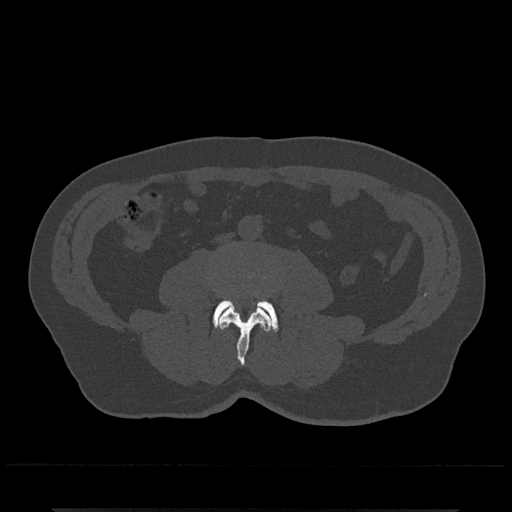
CT including the spine, one axial slice. Slice 193 of 797 in the series (ordered by position). Reconstruction kernel Br40s/3. 120 kVp. Bone window (W 1800 / L 400 HU). 0.5 mm slice thickness. 512 × 512 image matrix, field of view 393 × 393 mm. Patient: male, 67 years. From the clinical record (not read from this slice): primary cancer: prostate.
Annotated regions visible in this slice (semi-automatic segmentation, software-assisted and operator-edited):
- L3 vertebra: bounding box (x1, y1, x2, y2) in pixels: (218, 306, 272, 365)
- L4 vertebra: (213, 299, 279, 331)